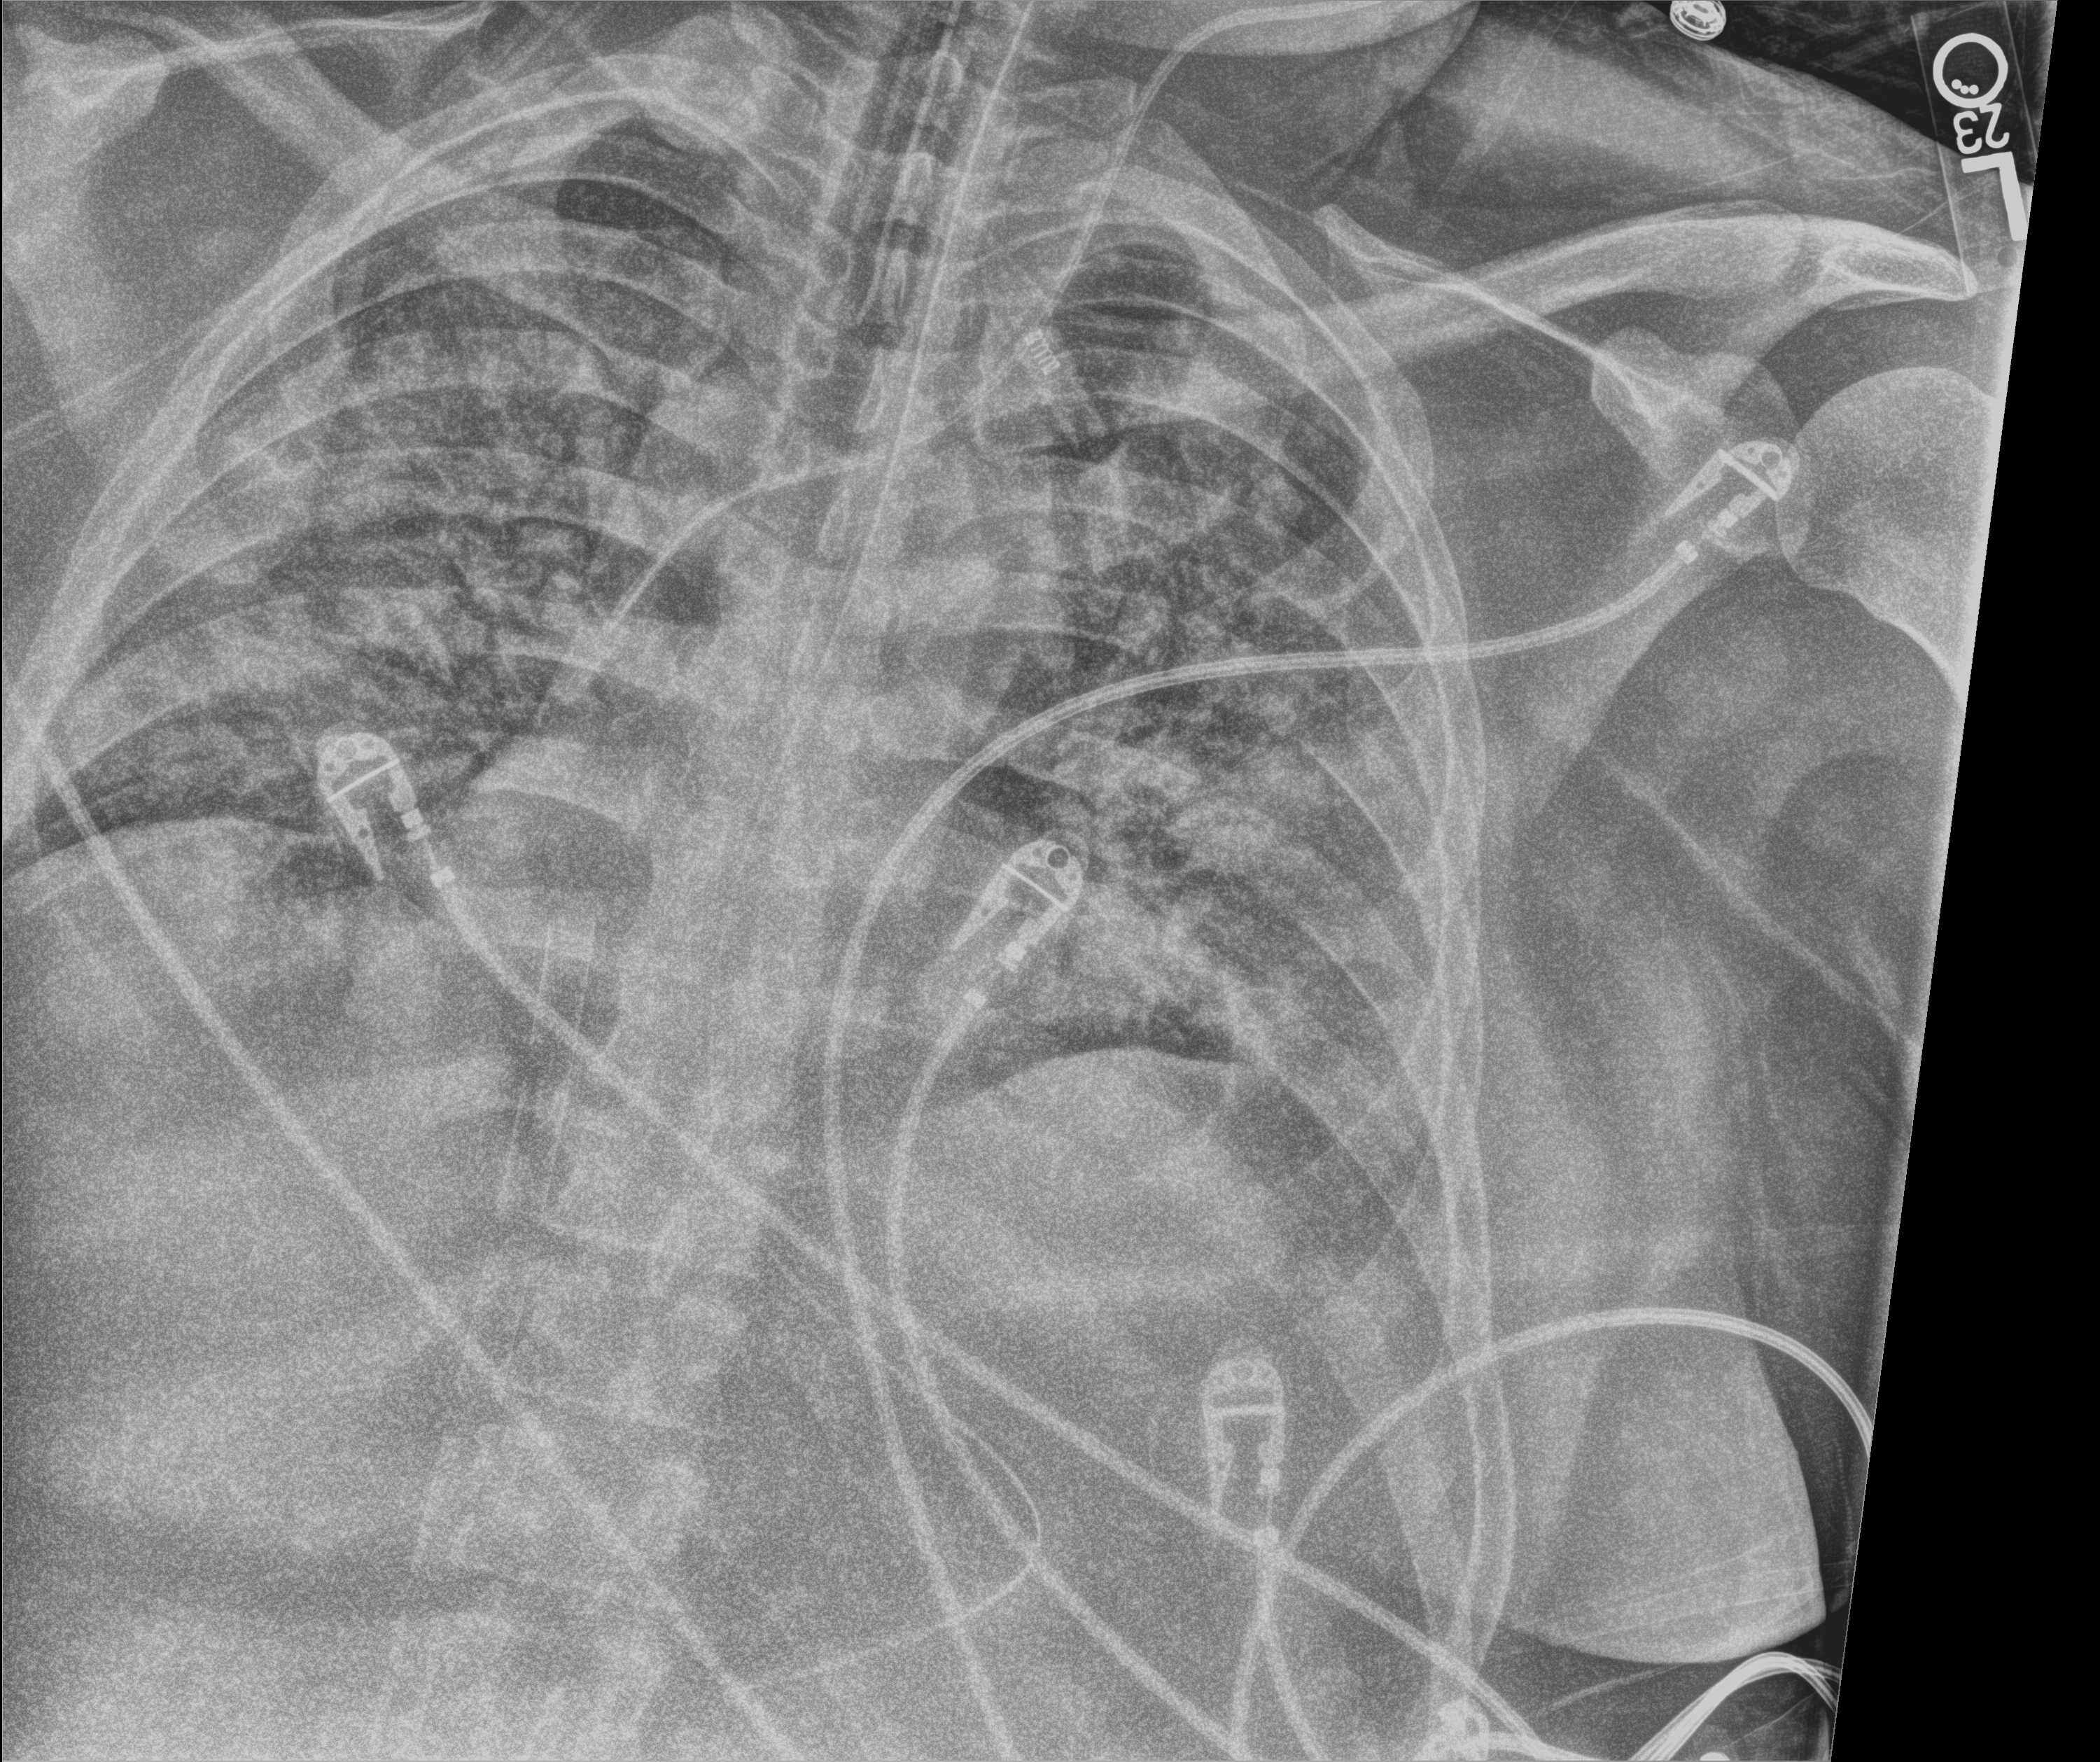
Chest X-ray (portable). Patient hospitalised with COVID-19, aged 18–59 years.
Admission-level facts for this patient (not findings on this image; timing relative to this image not recorded):
- admitted to intensive care during this hospital stay: yes